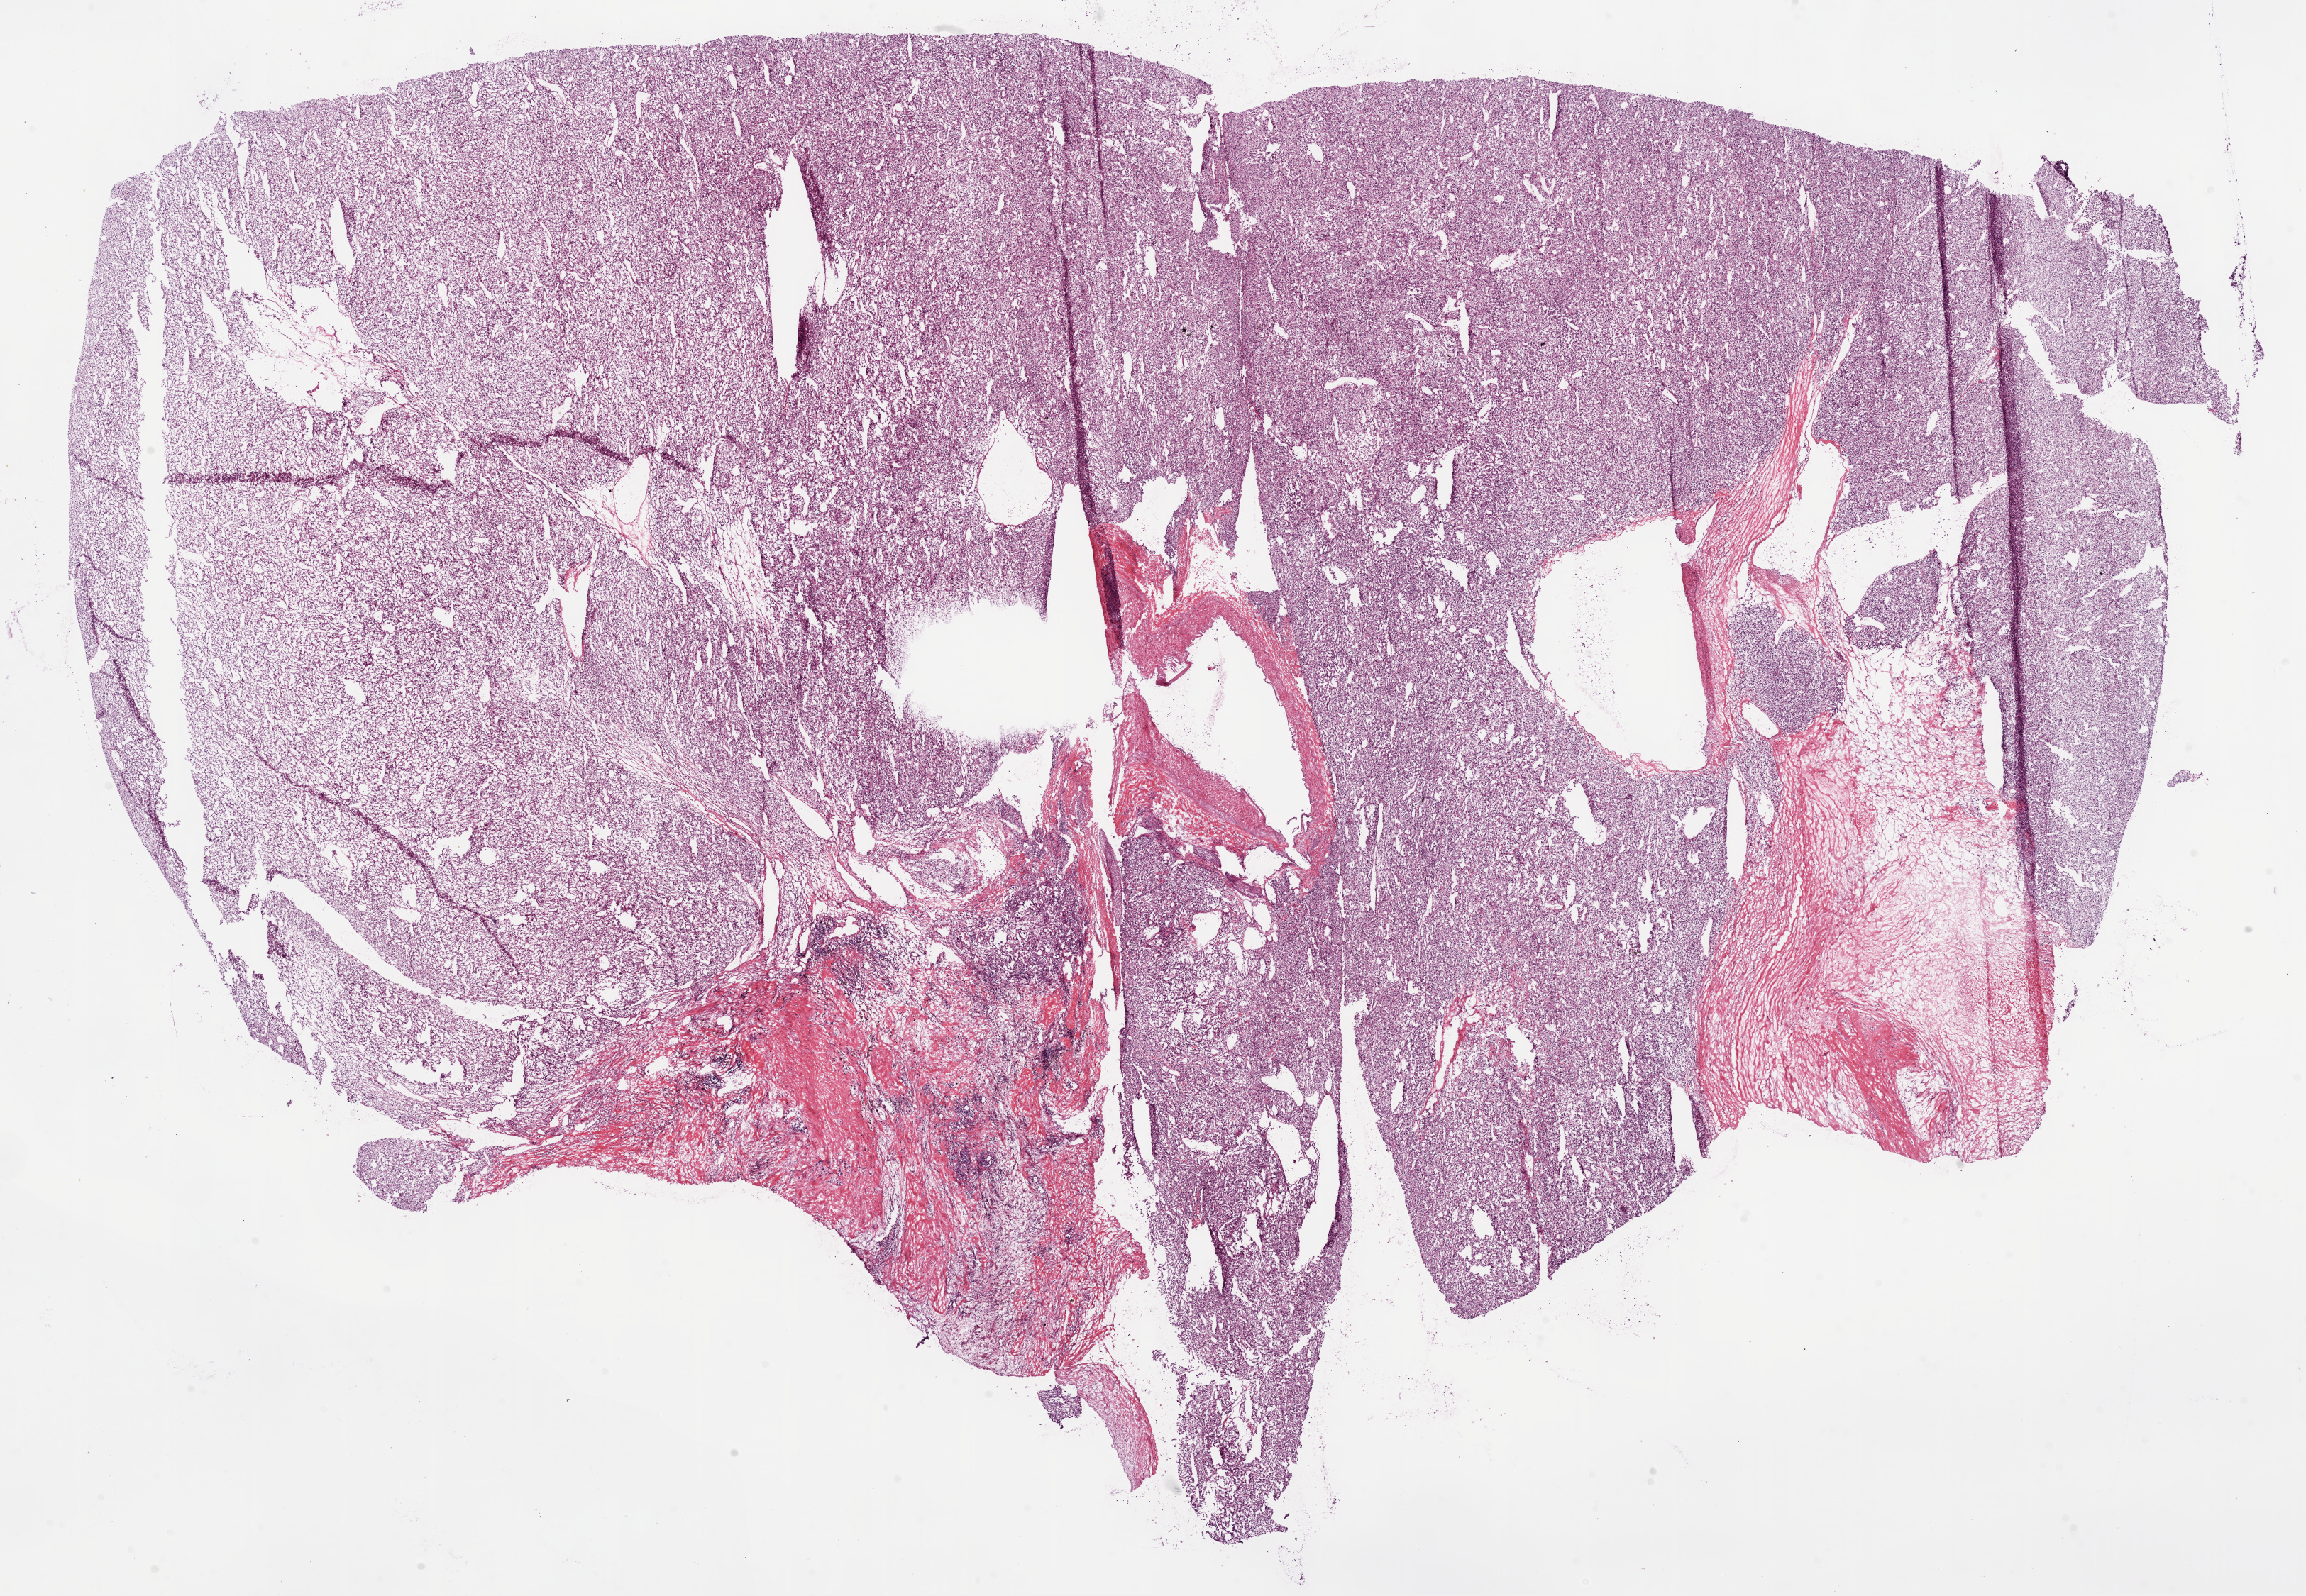
Digitized H&E tissue section (whole slide) — low-resolution overview of the scanned area, about 26.1 x 18.1 mm; frozen section from the bottom of the tissue portion; kidney, primary tumour sample. Male patient; age at initial diagnosis 58 years. Histologic grade: G3 (poorly differentiated). Pathologist review of this section (percent, as recorded): tumour cells 85%, tumour nuclei 85%, normal cells 0%, stromal cells 15%, necrosis 0%.
AJCC pathologic stage: IV. Pathologic diagnosis: Clear cell adenocarcinoma, NOS. TNM: T4 N0 M1.